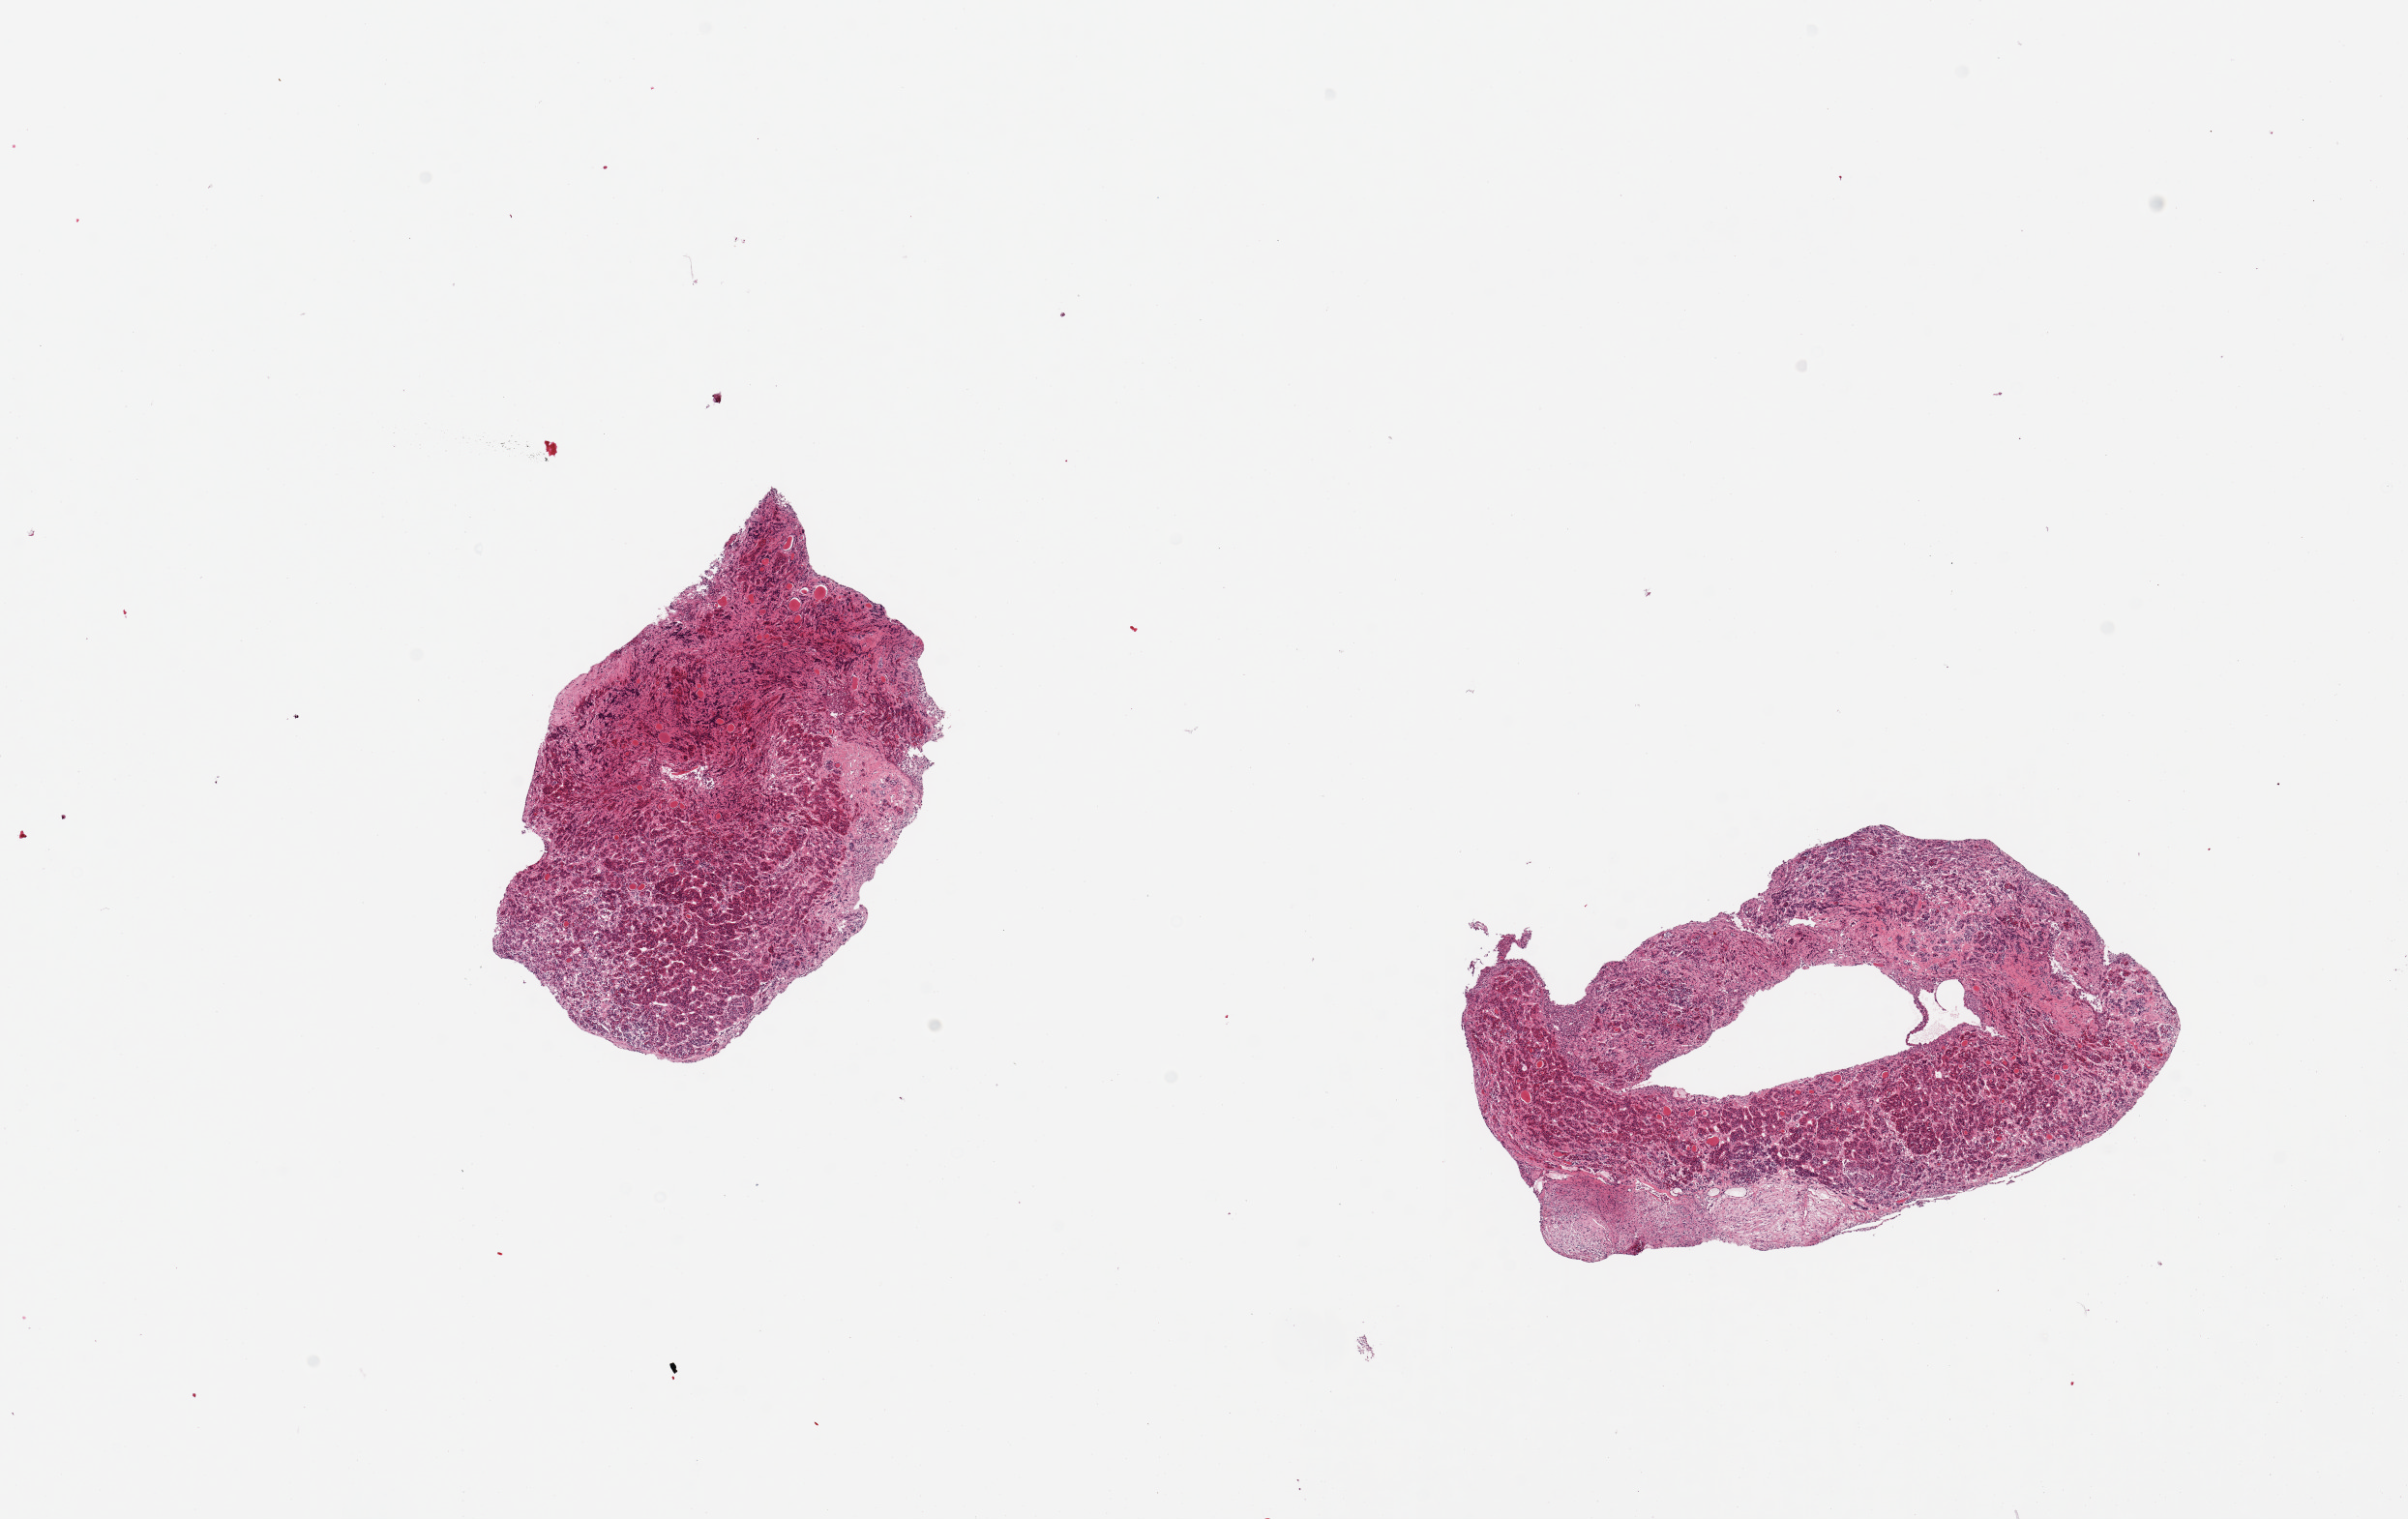
Haematoxylin and eosin whole-slide image, low-resolution overview of the scanned area, about 19.7 x 12.4 mm (acquisition: 20x scan). PAXgene-fixed paraffin-embedded (PFPE) section. Target tissue: pituitary. Donor tissue sample. Donor: male.
Review note (as recorded): 2 pieces, moderately autolyzed, one with small nubbin of neurohypophysis (~2x0.5mm); rest adenohypophysis.